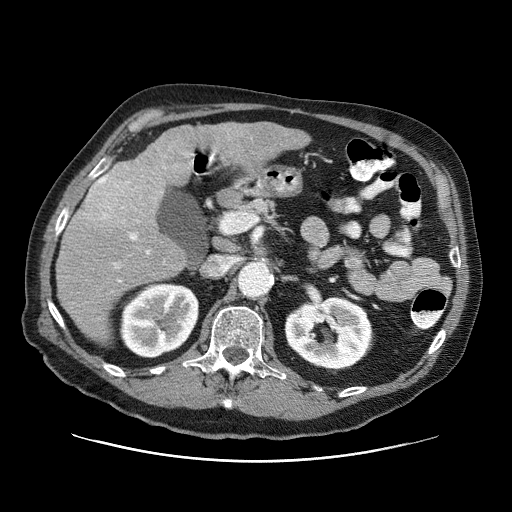
Contrast-enhanced abdominal CT (liver protocol), one axial slice. Slice 33 of 87 in the series (ordered by position). Reconstruction kernel STANDARD. 120 kVp. One of 3 acquisitions stored at this slice position. Soft-tissue window (W 400 / L 40 HU). 512 × 512 image matrix, field of view 400 × 400 mm. From the clinical record (not read from this slice): diagnosis: hepatocellular carcinoma (patient treated with transarterial chemoembolisation; whether this scan precedes or follows treatment is not stated here); TNM stage (as recorded): Stage-IIIA; Child-Pugh class: A; tumour differentiation: well differentiated.
Annotated regions visible in this slice (semi-automatic segmentation, software-assisted and operator-edited):
- liver parenchyma outside the tumour (the mass and vessels are separate outlines, so this box may not span the whole liver): bounding box [x1, y1, x2, y2] px = [56, 122, 310, 342]
- mass: [78, 150, 167, 229]
- liver vessels: [103, 153, 214, 282]